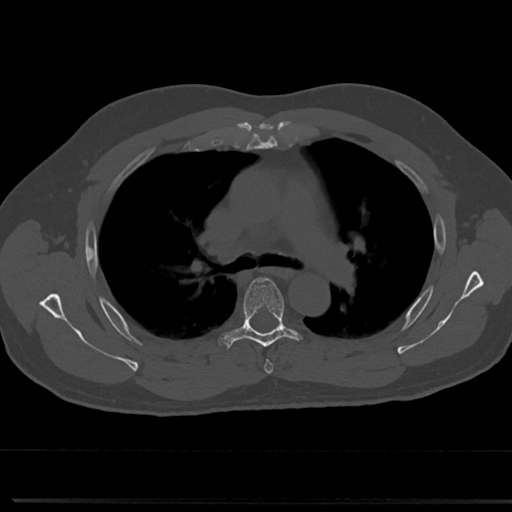
CT including the spine, one axial slice; position 504 of 817 along the scan axis; 120 kVp; bone window (W 1800 / L 400 HU); 0.5 mm slice thickness; 512 × 512 image matrix, field of view 355 × 355 mm. Patient: male, 61 years. Case-level facts recorded for this patient, not image findings: primary cancer: prostate.
Structures marked on this image (semi-automatically segmented with operator editing):
- T4 vertebra: bounding box [x1, y1, x2, y2] px = [263, 348, 273, 374]
- T5 vertebra: [218, 276, 310, 352]